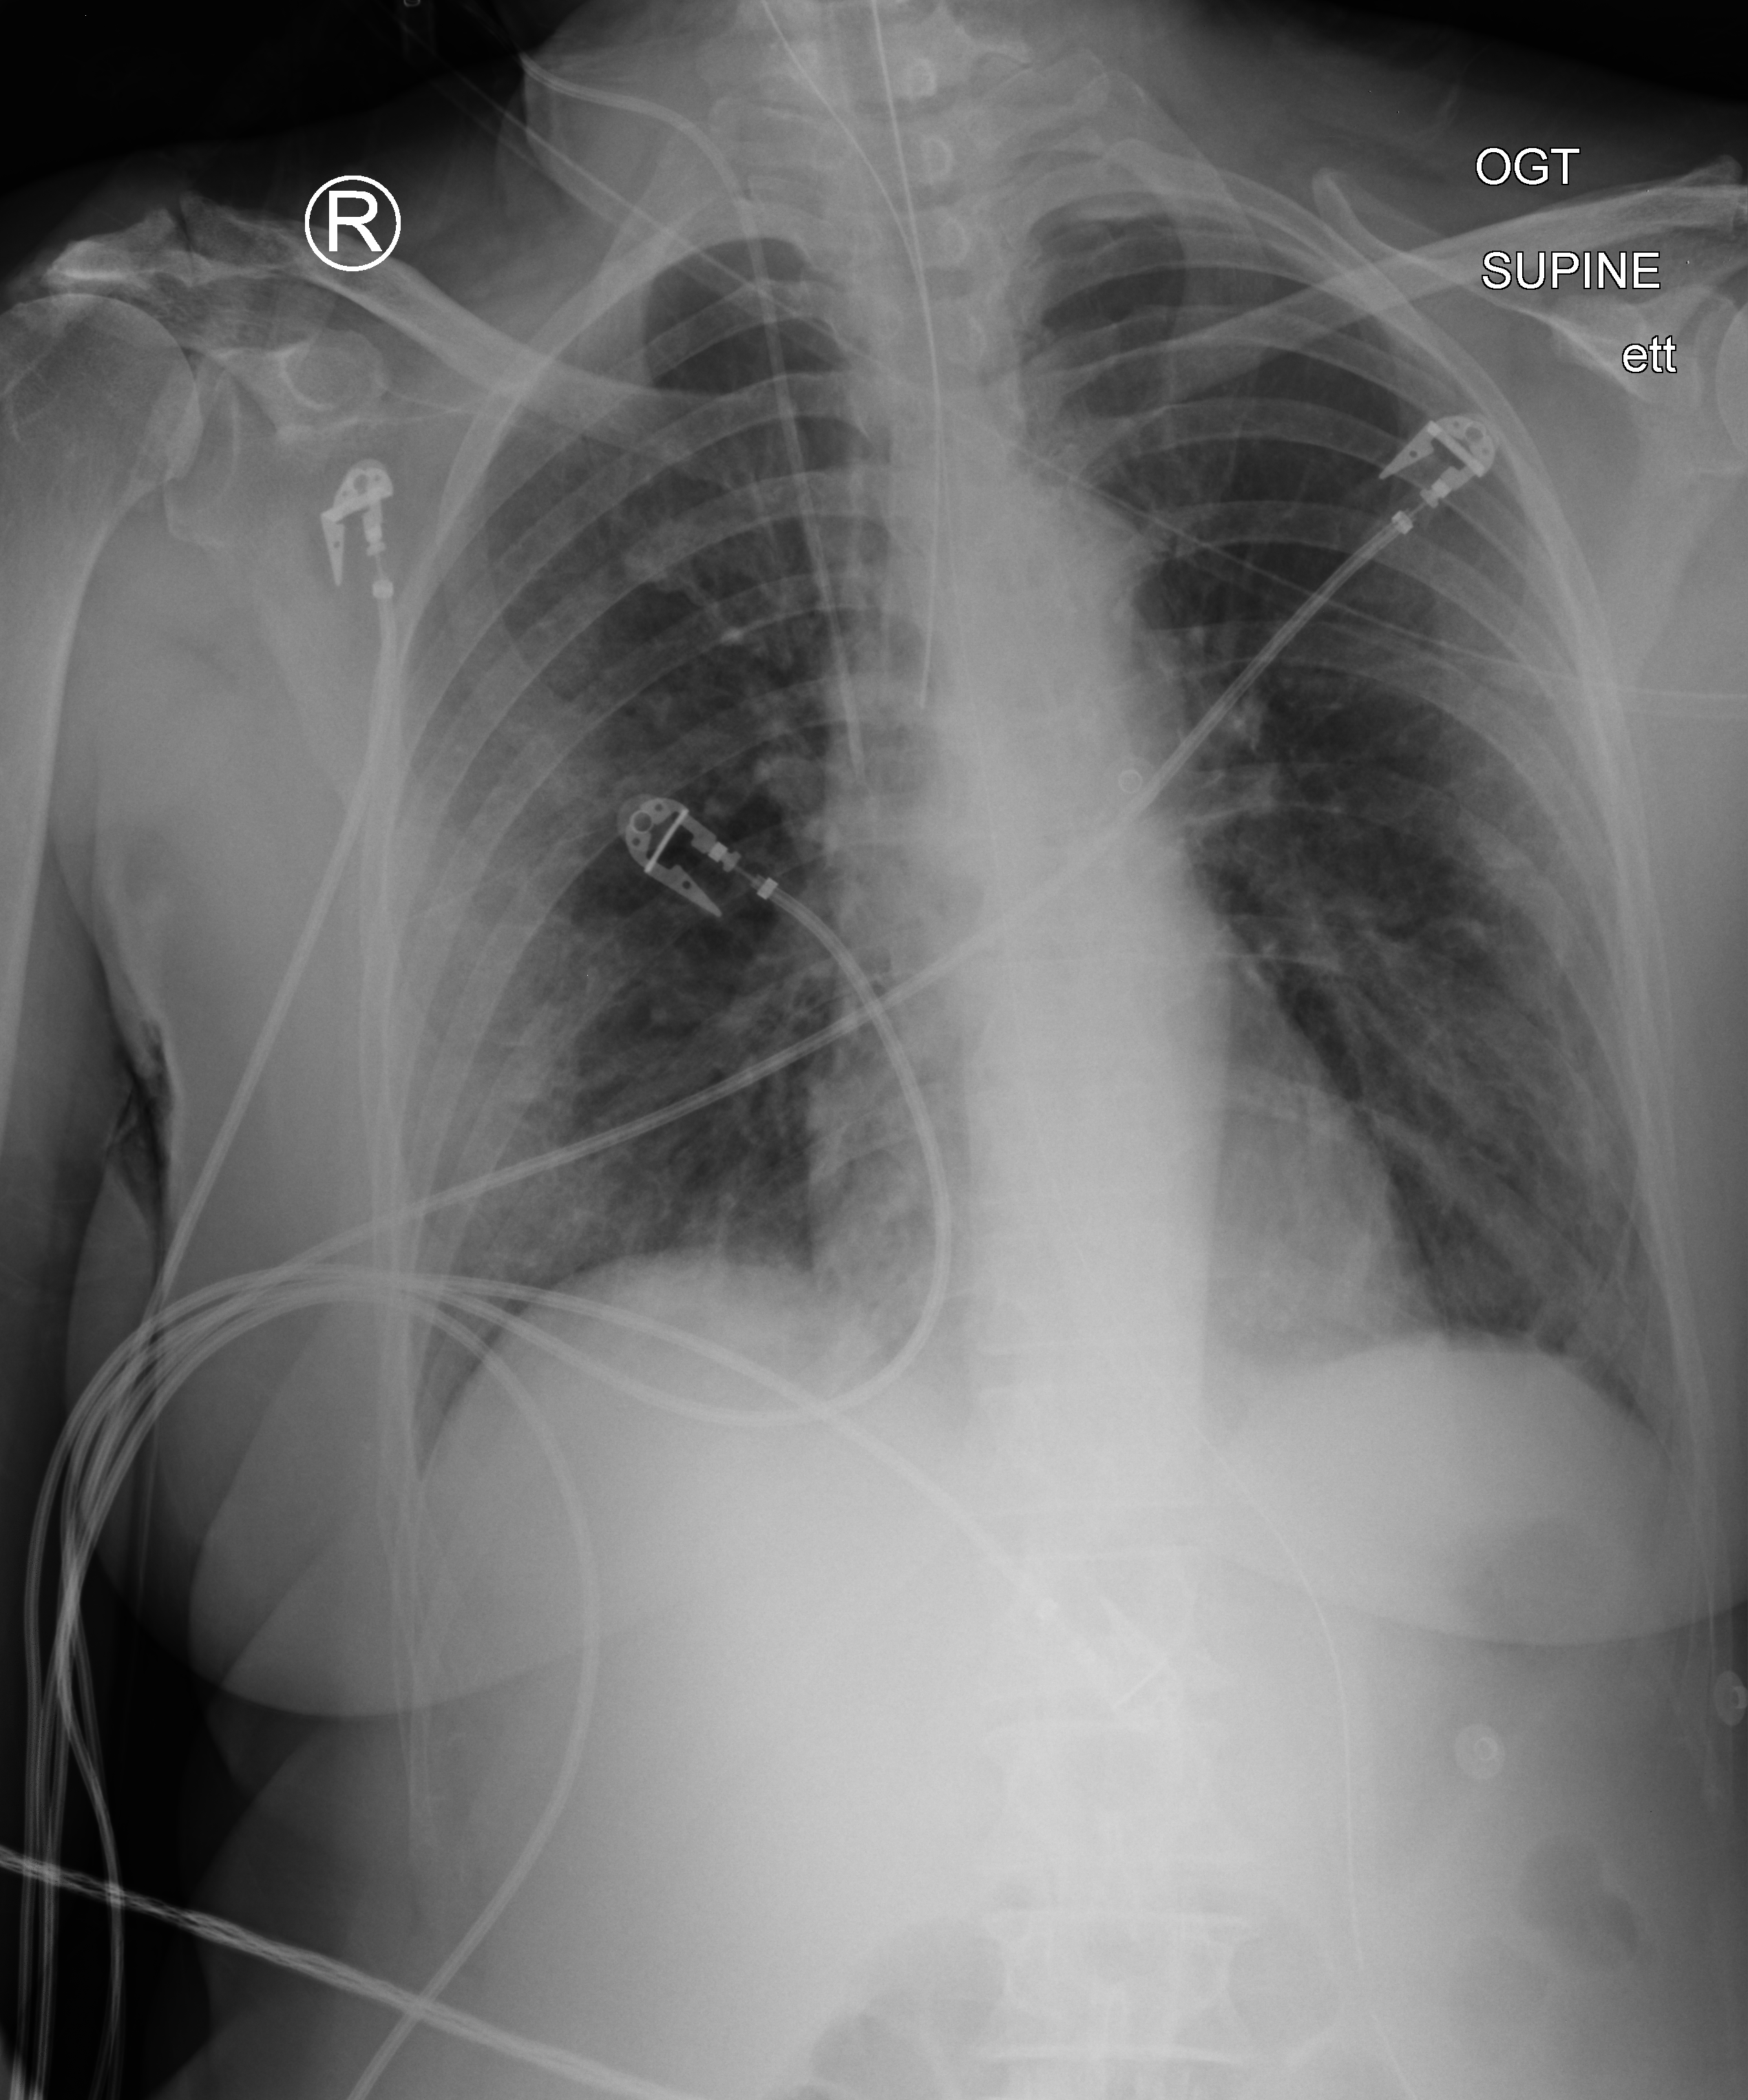
Portable chest radiograph; anteroposterior (AP) projection. Patient hospitalised with COVID-19; female, aged 60–74 years.
Hospital-stay facts (about this admission, not read from this image; timing relative to this image not recorded):
- admitted to intensive care during this hospital stay: yes